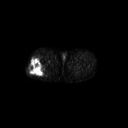
FDG PET of an extremity soft-tissue mass (from a PET/CT study), one axial slice; position 254 of 267 along the scan axis; 3.27 mm slice thickness; 128 × 128 image matrix. Male patient, age 43 years. From the clinical record (not read from this slice): histological type: poorly differentiated synovial sarcoma; grade: high; site of the primary tumour: right buttock.
Outlined on this slice (expert contour drawn on MRI and transferred to this co-registered scan by the dataset authors):
- gross tumour volume including surrounding oedema: box from (x=28, y=57) to (x=46, y=76) px
- gross tumour volume (mass): (x=28, y=57)–(x=46, y=76)